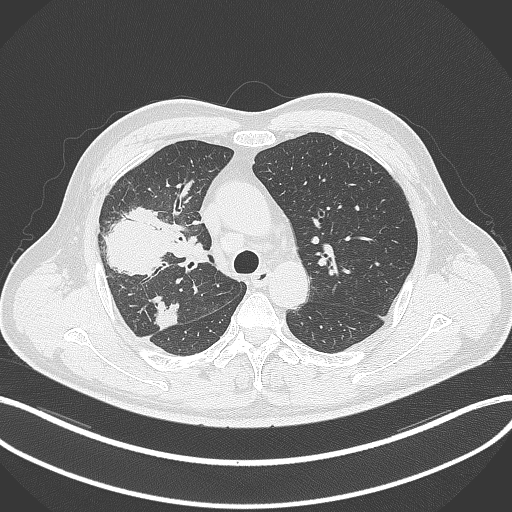
Chest CT, one axial slice. Slice 229 of 348 in the series (ordered by position). Reconstruction kernel B70f. 120 kVp. Lung window (W 1500 / L -600 HU). 1 mm slice thickness. 512 × 512 image matrix, field of view 400 × 400 mm. Patient: male, 55 years. From the clinical record (not read from this slice): clinical TNM (as recorded): T3 N2 M1.
Outlined on this slice (bounding box drawn by a radiologist):
- lung tumour (recorded histology: adenocarcinoma): box from (x=100, y=200) to (x=178, y=278) px